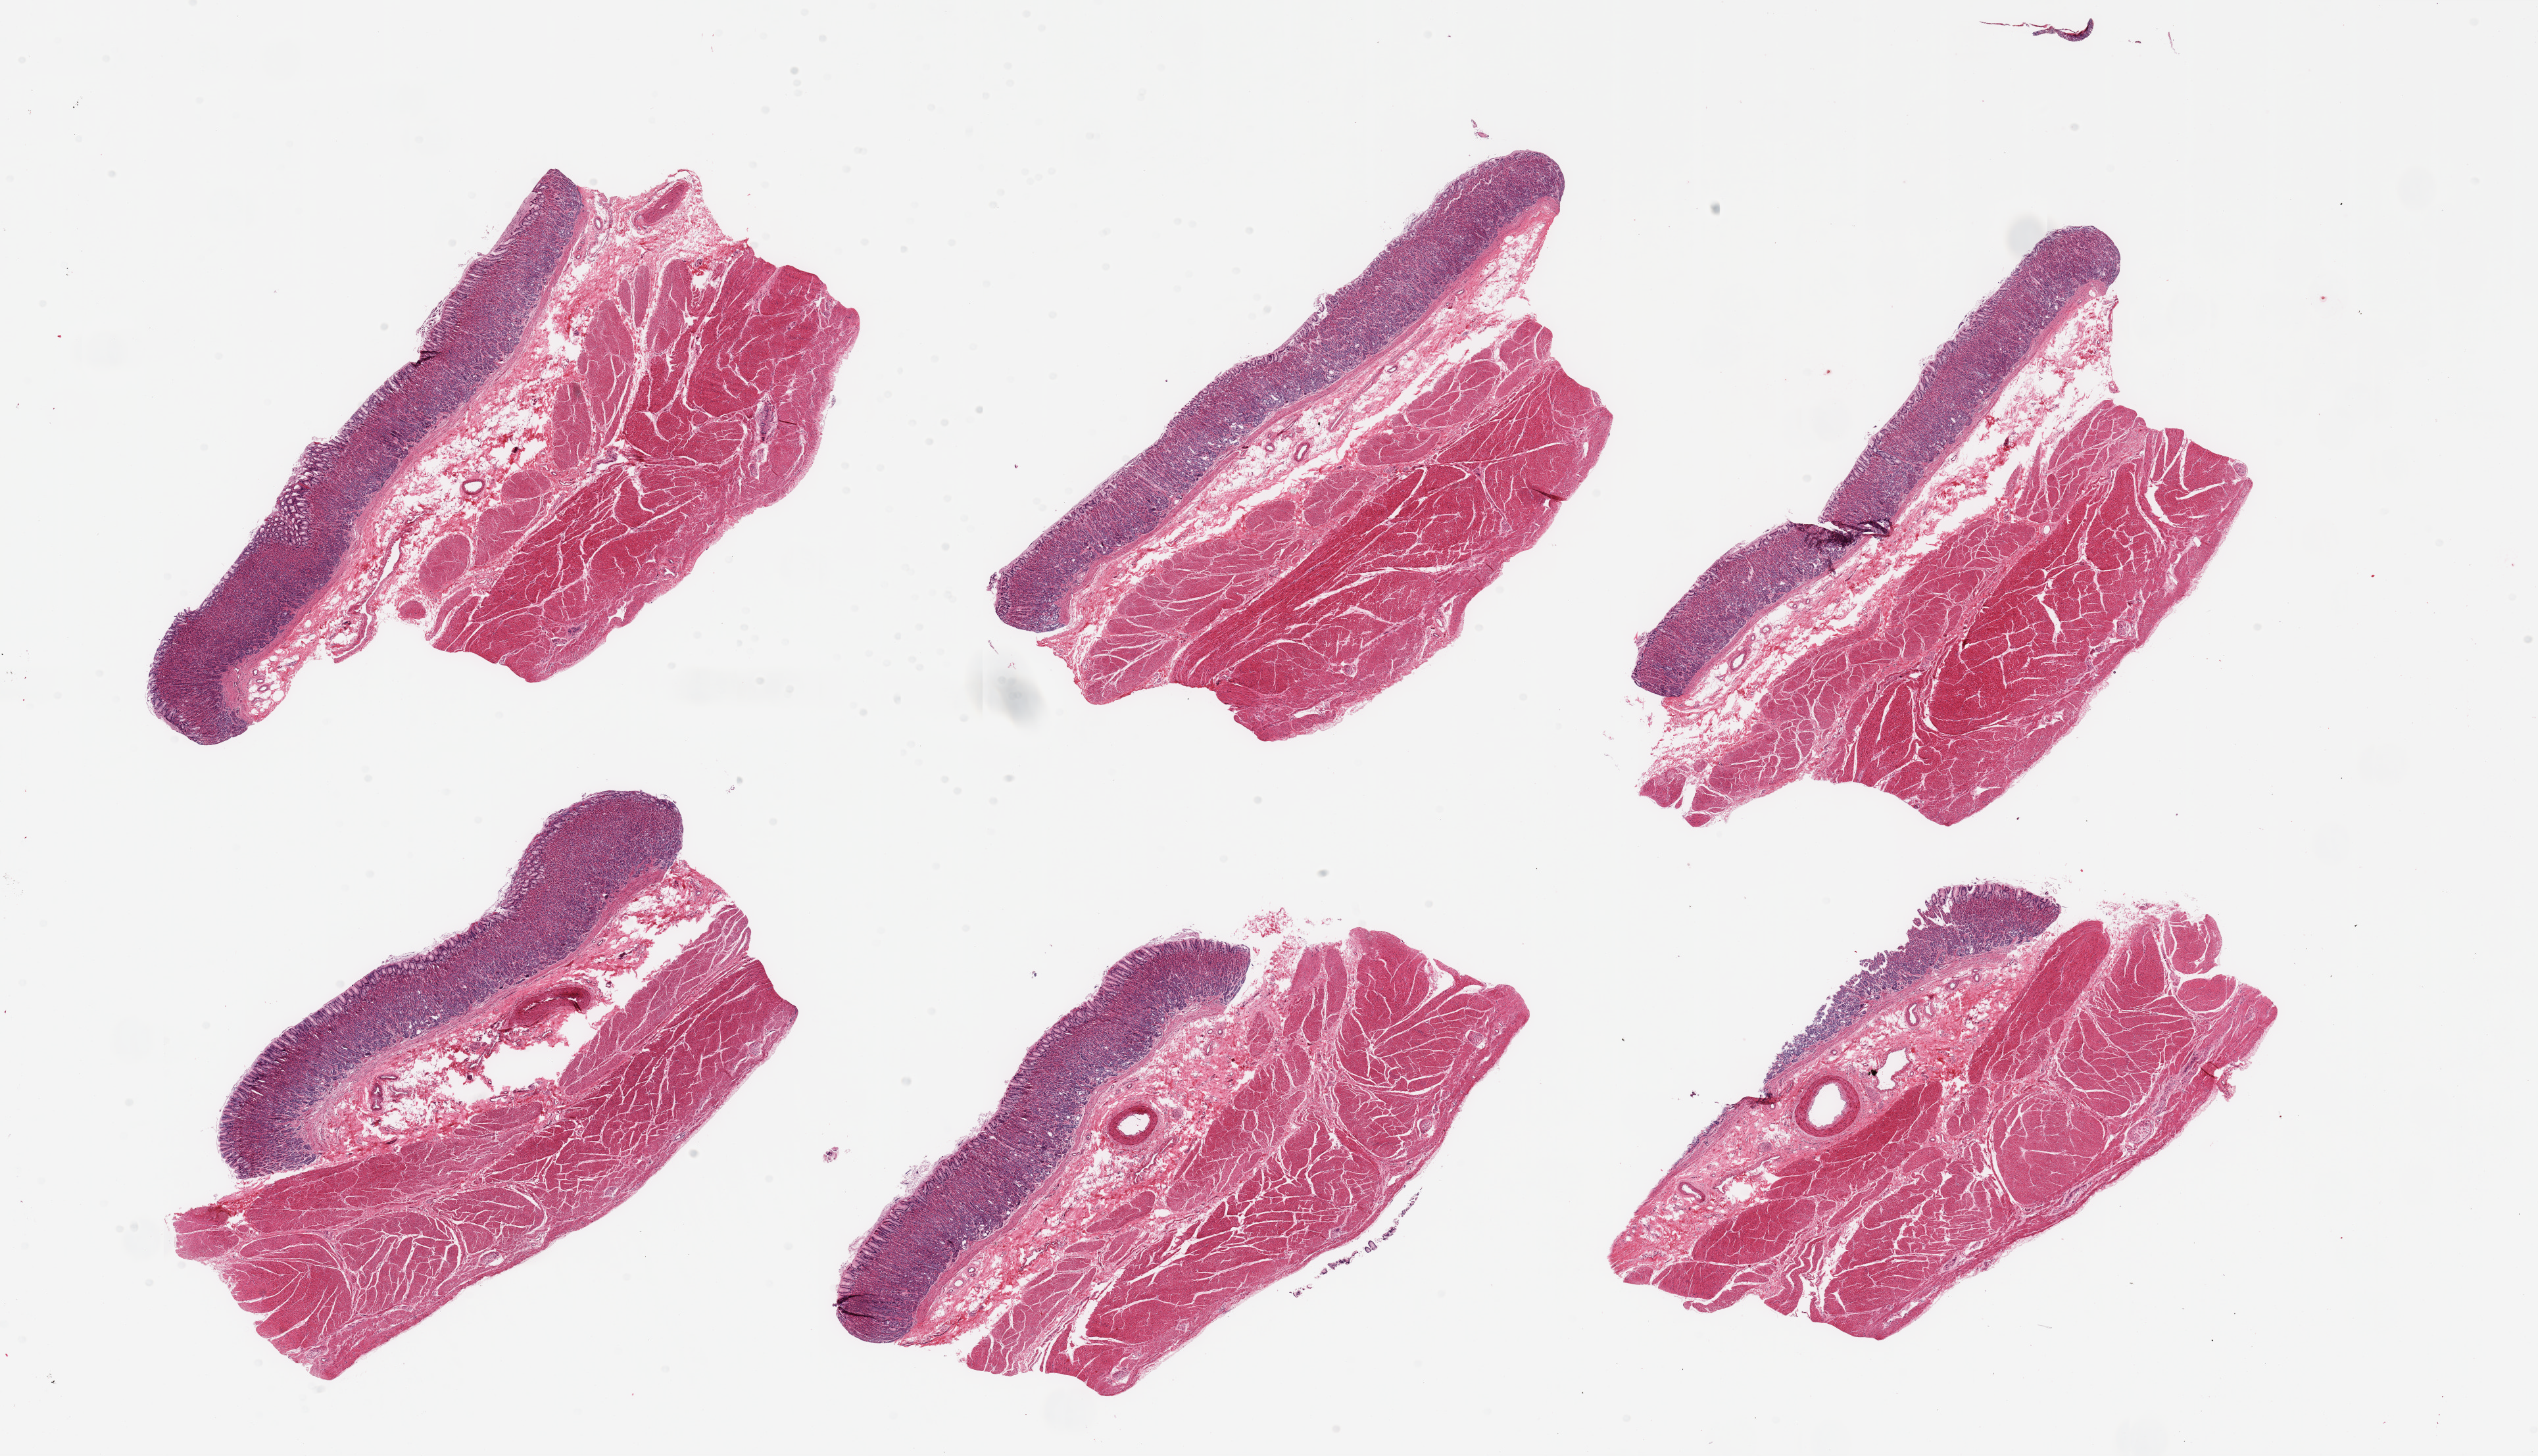
Haematoxylin and eosin whole-slide image, brightfield, shown as a low-resolution overview of the whole scanned area (about 30.5 x 17.5 mm); PAXgene-fixed paraffin-embedded (PFPE) section; target tissue: stomach; tissue donor sample.
* reviewer comment on this tissue sample: 6 pieces, well - preserved mucosa up to ~1.2mm, 30-25% thickness; Basal microcystic dilation or gastropathy